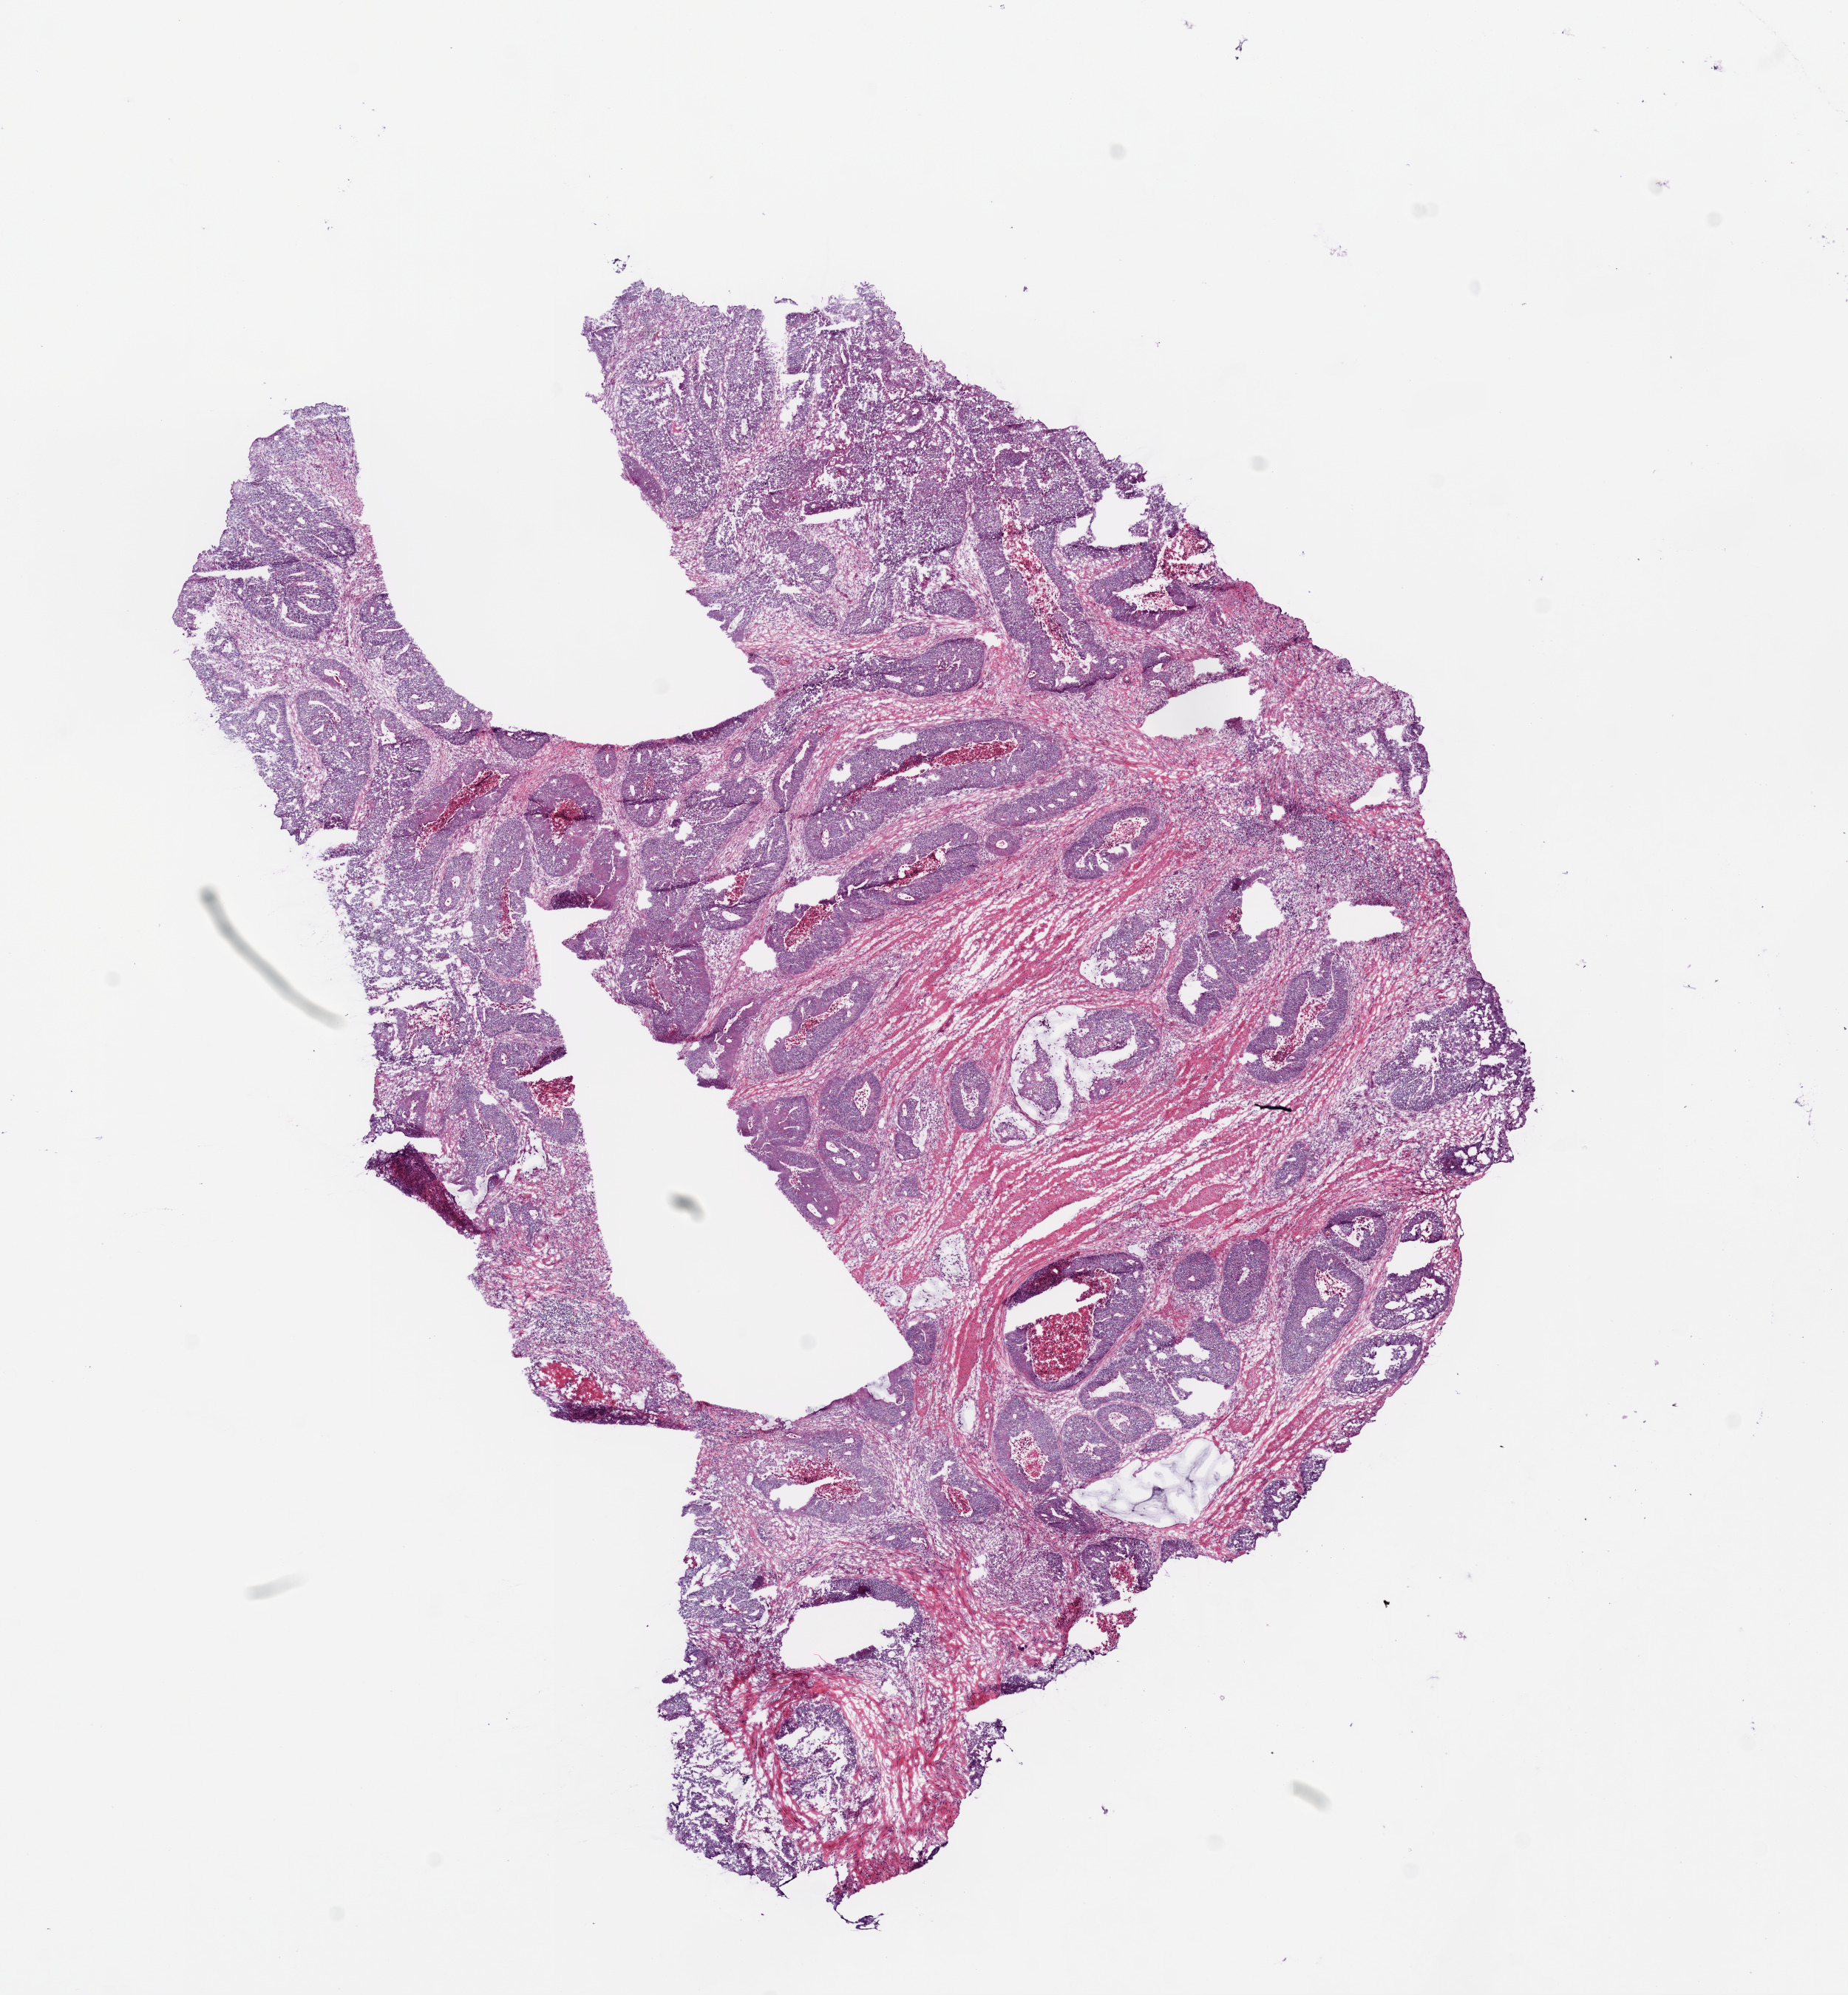
Whole-slide histology image, H&E — whole scanned area (about 10.0 x 10.8 mm, from a 20x scan) shown as a low-resolution overview, frozen section from the bottom of the tissue portion, sample: primary tumour, colon. Patient sex: female. Slide review estimates, as recorded: tumour cells 60%, tumour nuclei 70%, normal cells 0%, stromal cells 40%, necrosis 0%.
Pathologic diagnosis: Adenocarcinoma, NOS (ascending colon). Lymph nodes positive (case pathology): 0 of 15 examined. AJCC pathologic stage: IIA (6th edition).